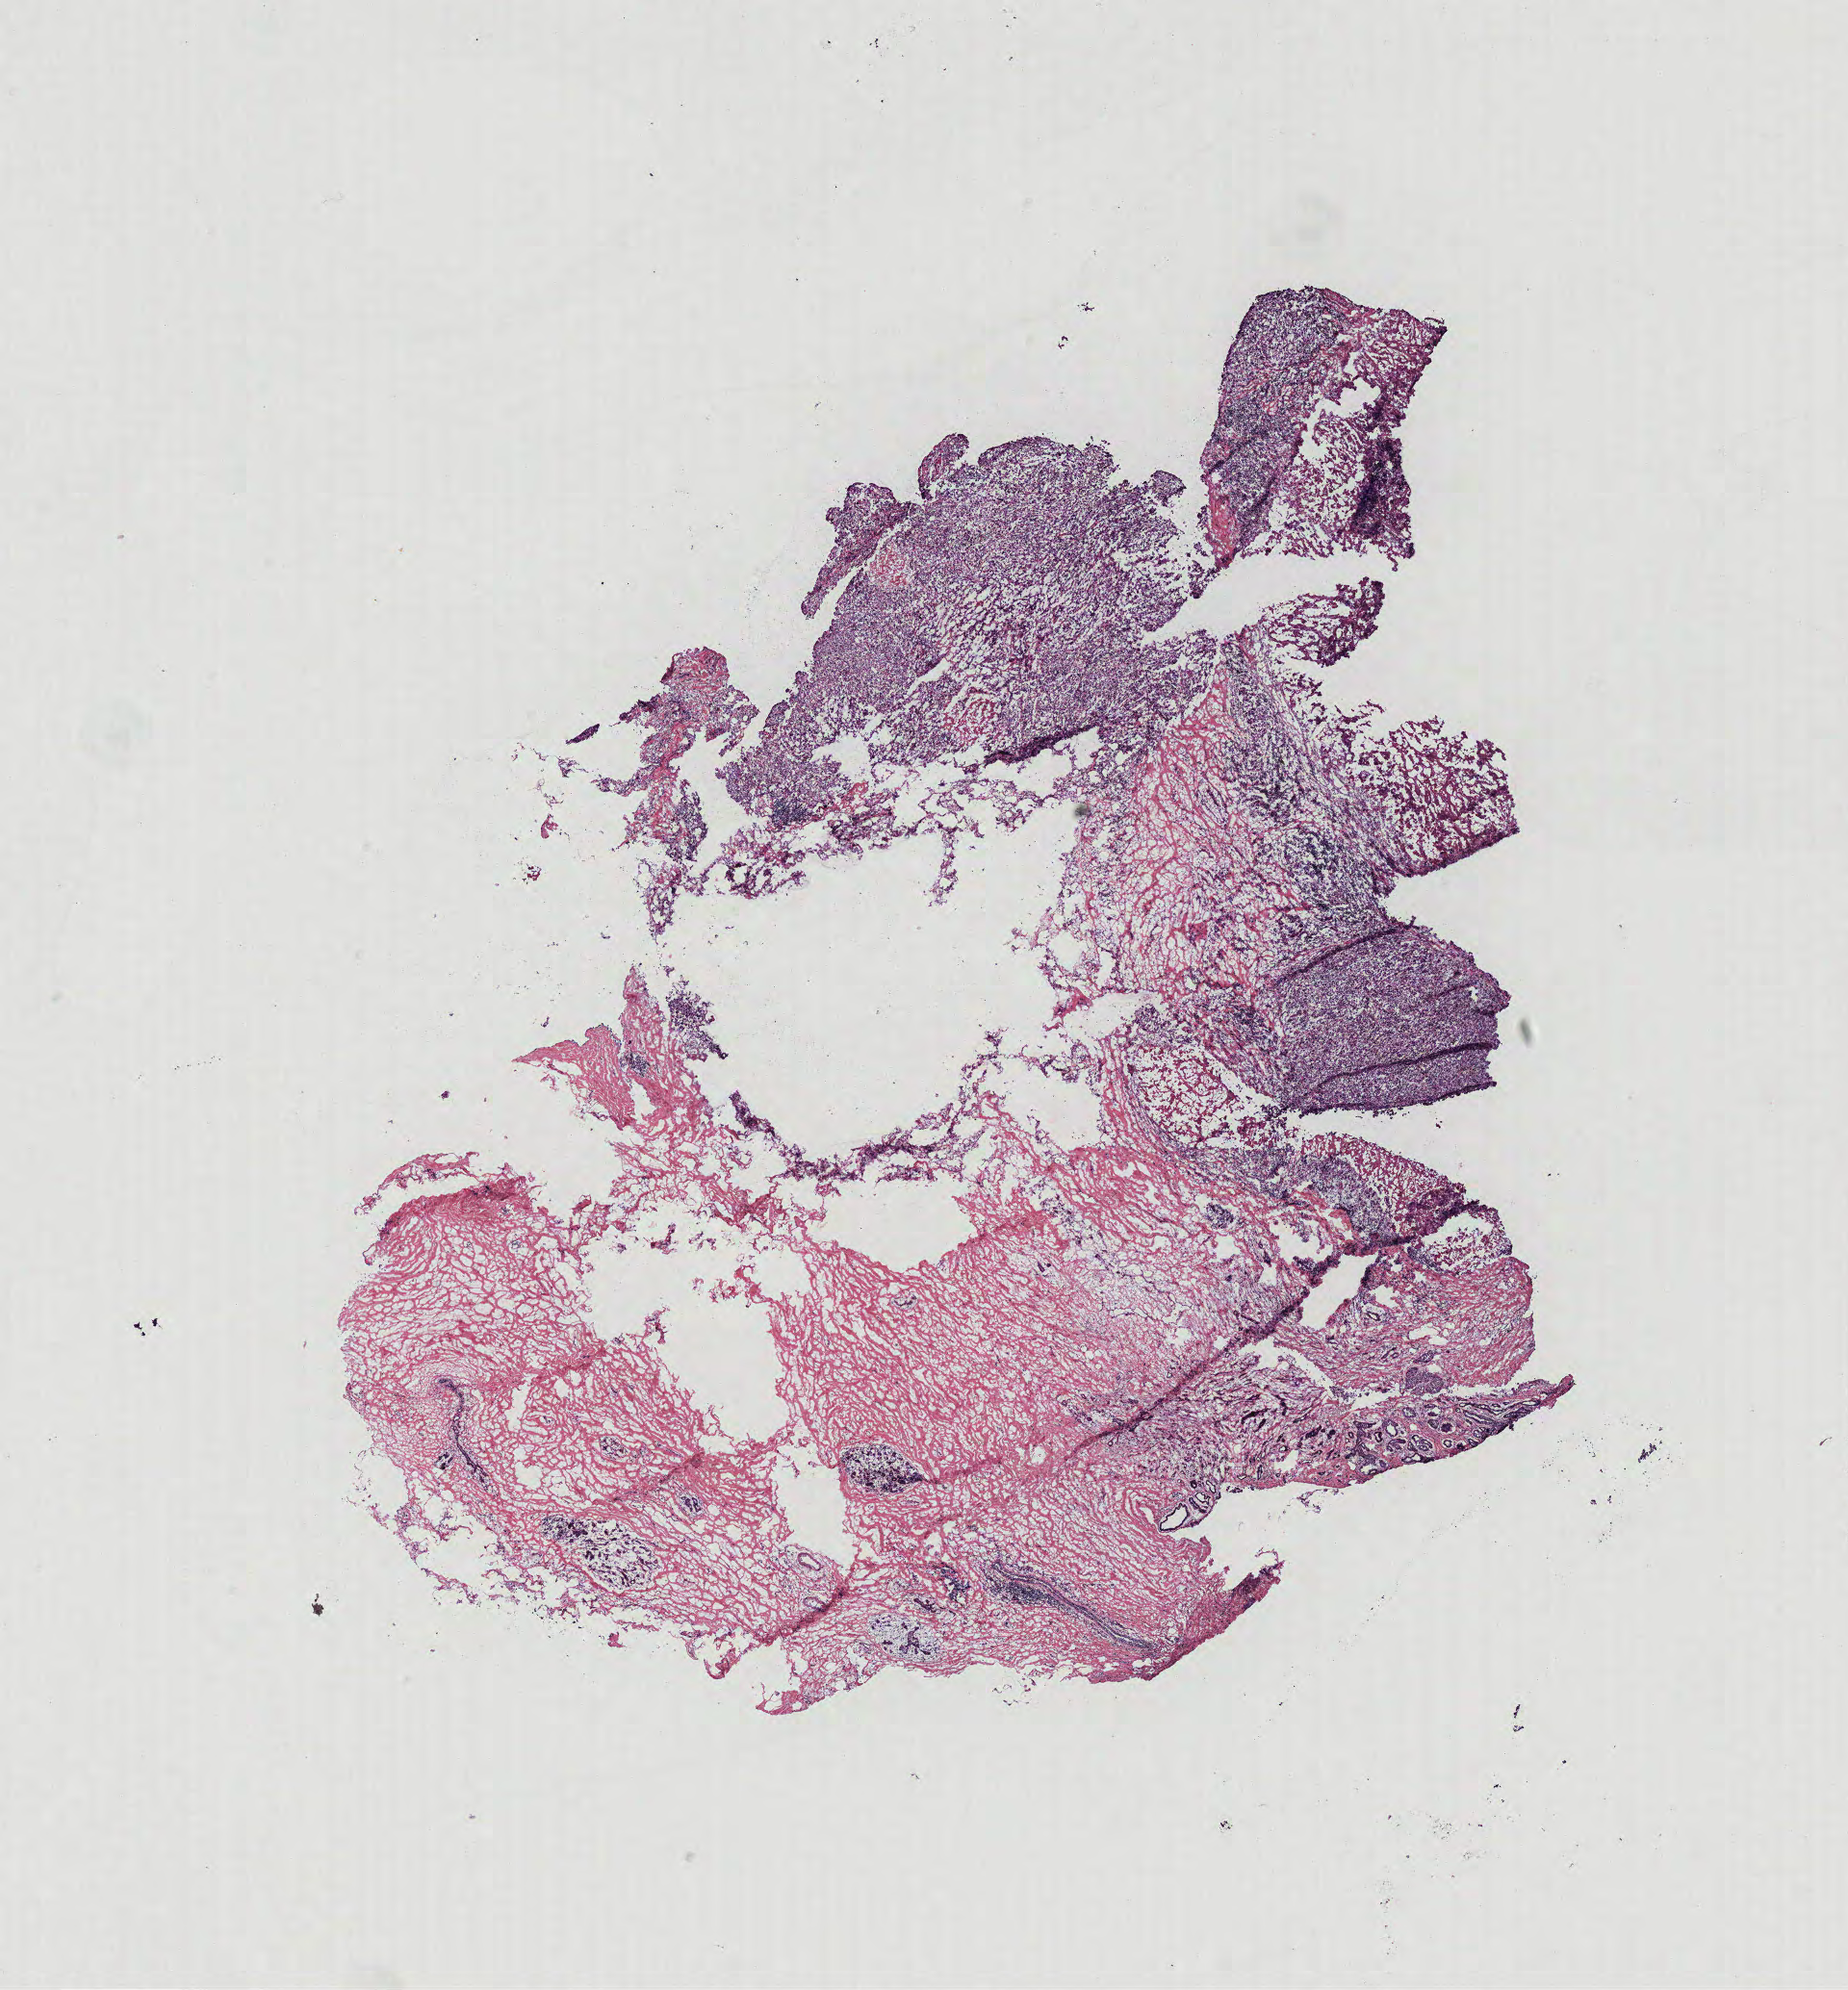
Whole-slide histology image, Hematoxylin and eosin (H&E) stained, low-resolution overview of the scanned area, about 15.4 x 16.6 mm (slide scanned at 40x); breast, tissue type not recorded.
- patient diagnosis (cohort enrolment): breast cancer (breast)